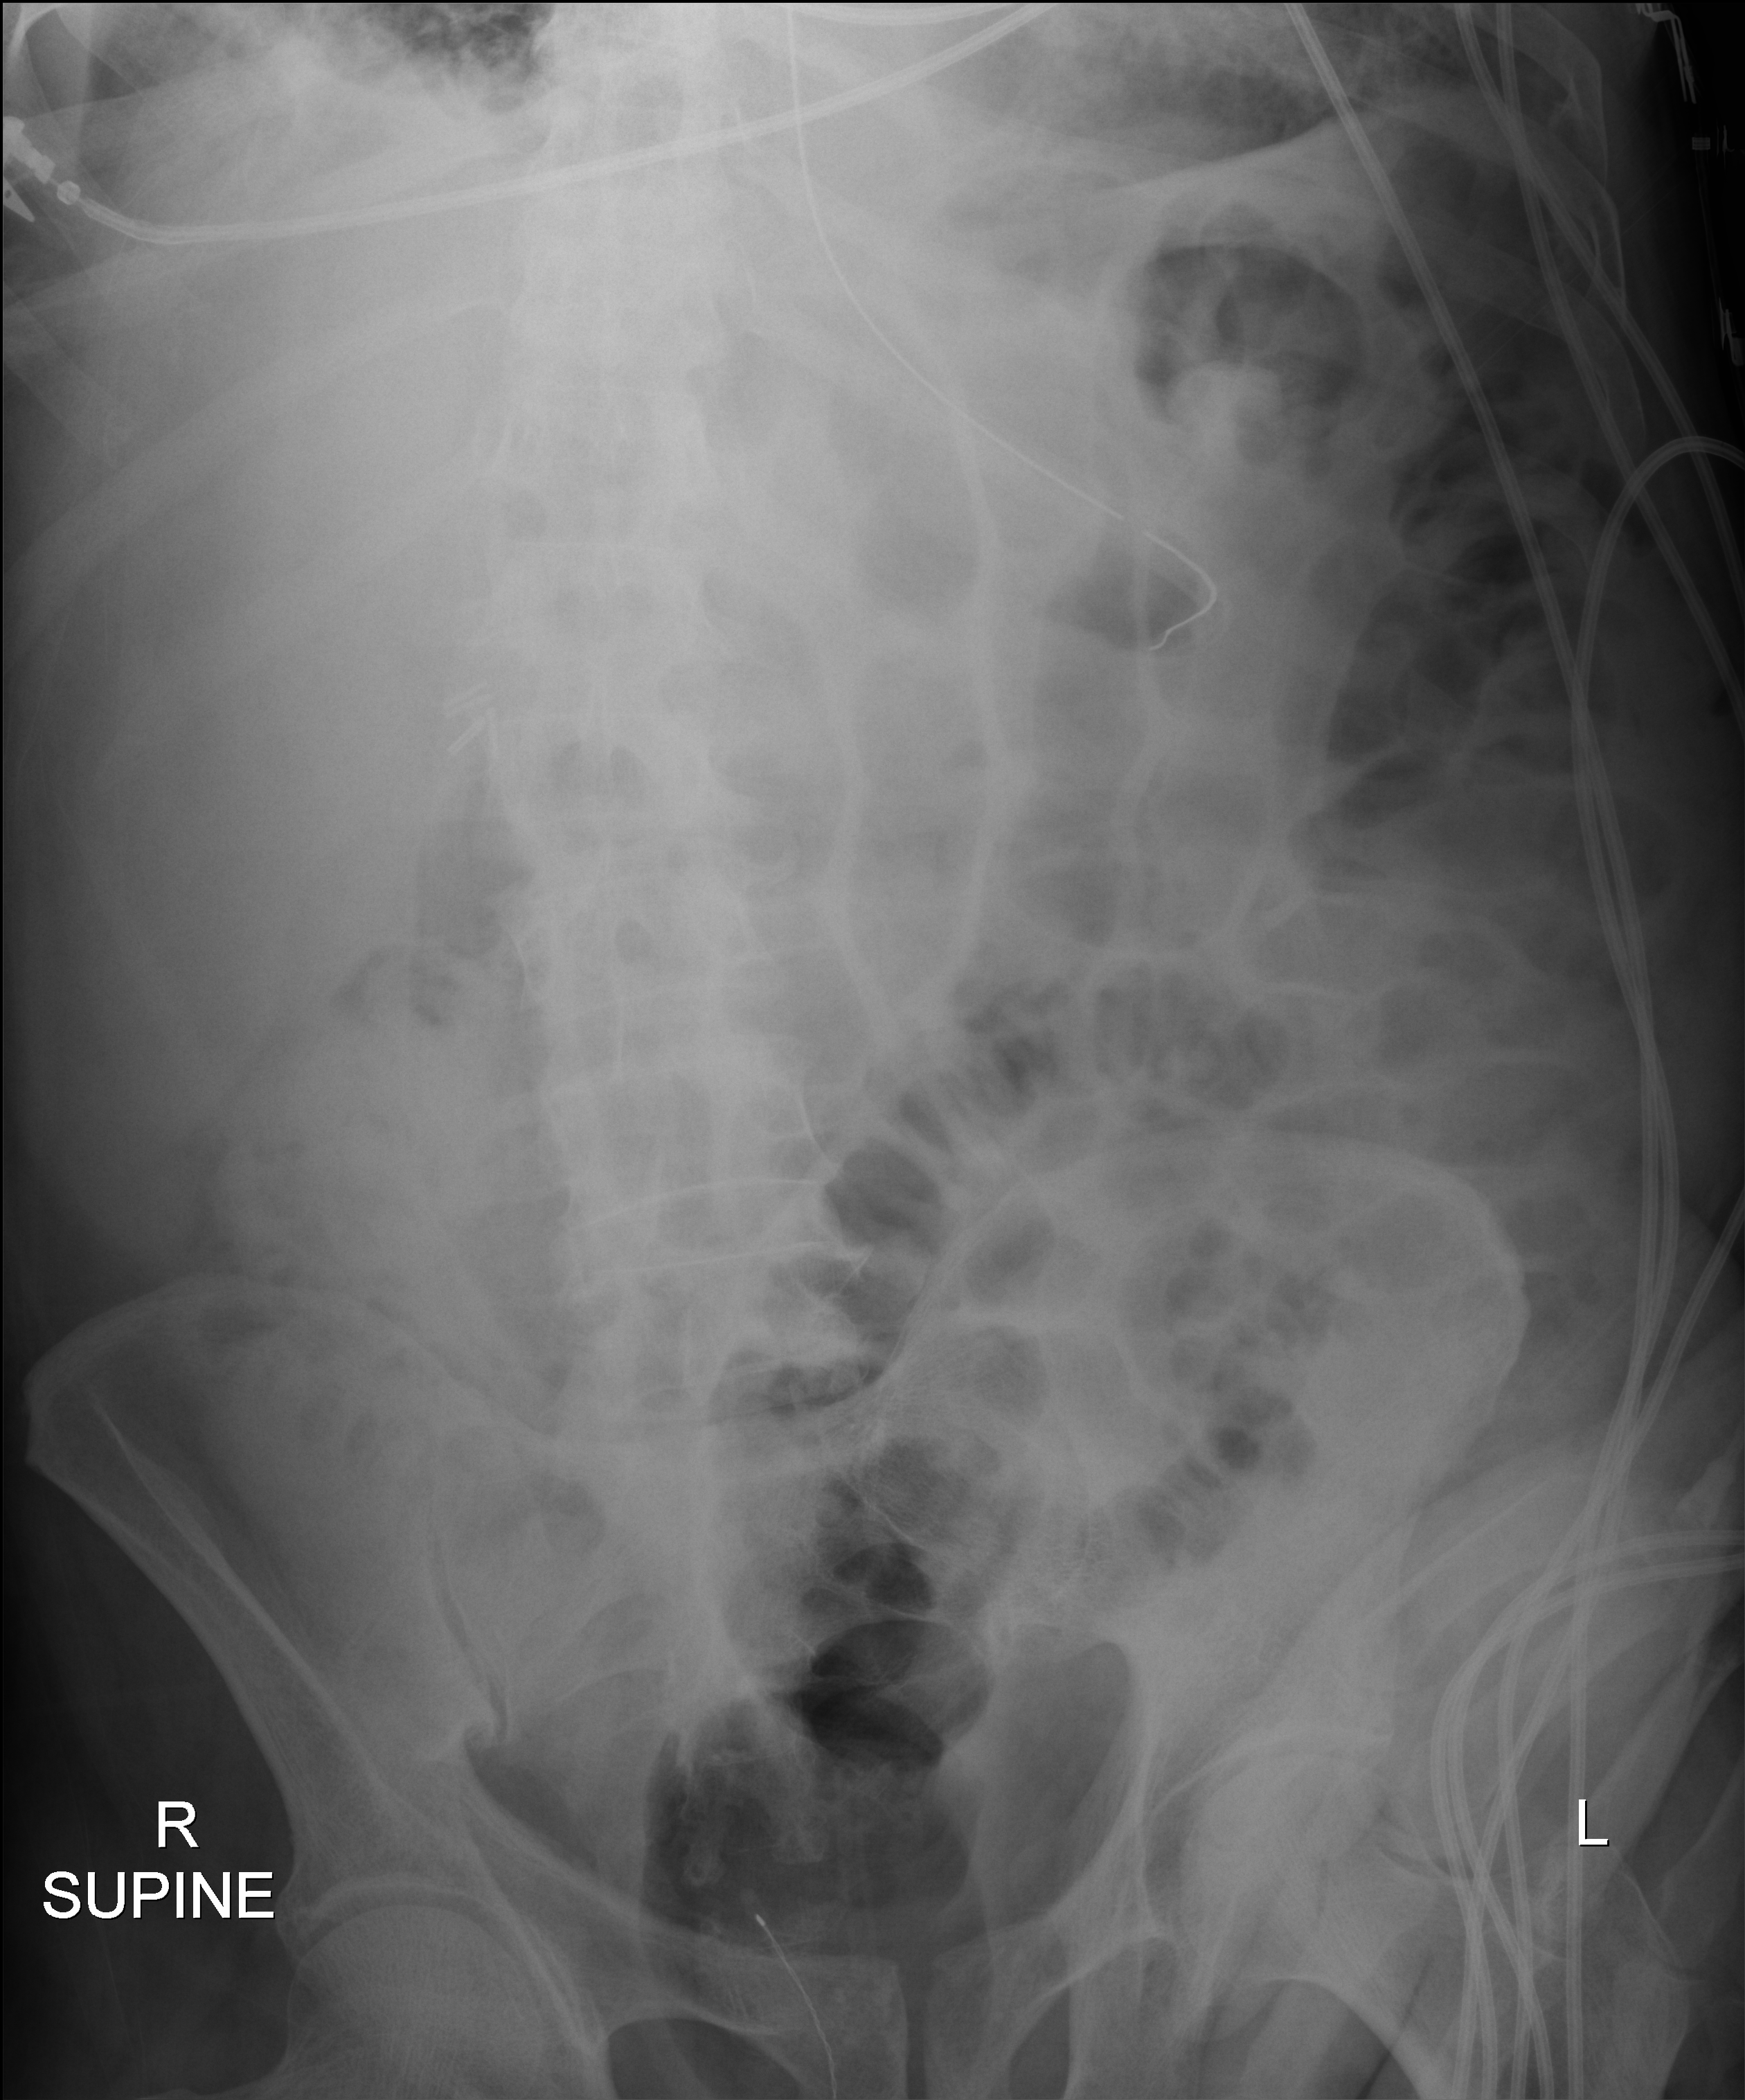
Bedside abdomen radiograph (digital radiography), anteroposterior (AP) projection. Male patient hospitalised with COVID-19, age 75–90 years.
Admission-level facts for this patient (not findings on this image; timing relative to this image not recorded):
- mechanically ventilated during this hospital stay: yes
- other chronic lung disease (admission record): yes